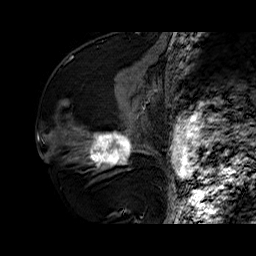
Breast MRI (dynamic contrast-enhanced), one sagittal slice. Slice 31 of 60 in the series (ordered by position). Dynamic contrast-enhanced series, time point 2 of 6 at this slice position (early post-contrast). 1.5 T. TE 6.4 ms, TR 32.7 ms. 256 × 256 image matrix, field of view 200 × 200 mm. Female patient. Case-level facts recorded for this patient, not image findings: setting: breast cancer imaged before/during neoadjuvant chemotherapy; receptor status: HR-positive, HER2-negative.
Annotated regions visible in this slice (semi-automatic segmentation, software-assisted and operator-edited):
- analysis volume of interest (the breast-tissue region the enhancement analysis was run in; not a lesion): bounding box <73,110,141,174> (left, top, right, bottom; pixels)
- tumour enhancement mask (voxels above the 100 % enhancement threshold inside the analysis volume of interest): <88,133,133,167>